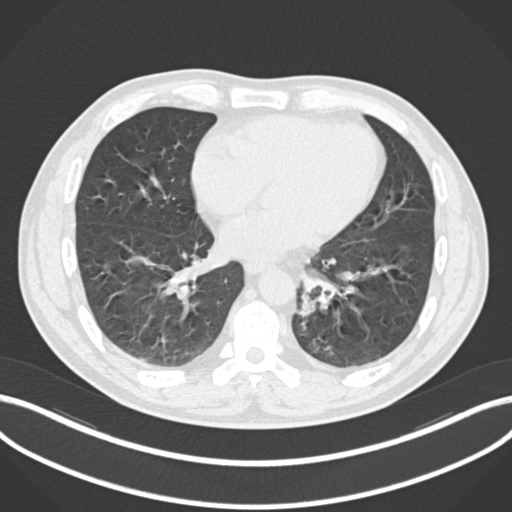
Chest CT, one axial slice. Position 75 of 223 along the scan axis. Reconstruction kernel B30f. 120 kVp. Lung window (W 1500 / L -600 HU). 512 × 512 image matrix. Male patient, age 50 years. Case-level facts recorded for this patient, not image findings: clinical TNM (as recorded): T2a N3 M0.
Annotated regions visible in this slice (rectangle marked by the reading radiologist):
- lung tumour (recorded histology: squamous cell carcinoma): box from (x=290, y=287) to (x=323, y=321) px